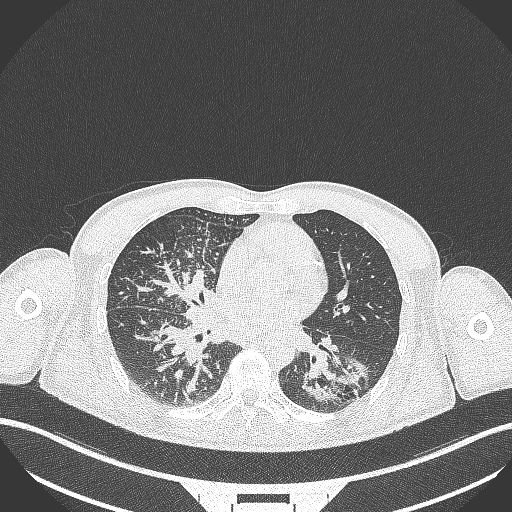
Chest CT, one axial slice; slice 149 of 348 in the series (ordered by position); reconstruction kernel B70f; 120 kVp; lung window (W 1500 / L -600 HU); 512 × 512 image matrix, field of view 400 × 400 mm. Patient: male, 49 years. From the clinical record (not read from this slice): clinical TNM (as recorded): T2b N1 M0.
Outlined on this slice (bounding box drawn by a radiologist):
- lung tumour (recorded histology: adenocarcinoma): bounding box [x1, y1, x2, y2] px = [296, 354, 365, 401]